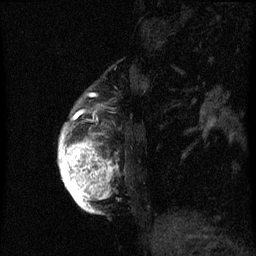
Breast MRI (dynamic contrast-enhanced), one sagittal slice. Slice 11 of 60 in the series (ordered by position). Dynamic contrast-enhanced series, image 2 of 3 at this slice position (ordered by acquisition). 1.5 T. TE 4.2 ms, TR 8 ms. 2 mm slice thickness. 256 × 256 image matrix, field of view 180 × 180 mm. Female patient, age 56 years.
Outlined on this slice (semi-automatic segmentation, software-assisted and operator-edited):
- analysis volume of interest (the breast-tissue region the enhancement analysis was run in; not a lesion): bounding box (x1, y1, x2, y2) in pixels: (58, 96, 119, 215)
- tumour enhancement mask (voxels above the 70 % enhancement threshold inside the analysis volume of interest): (58, 110, 113, 213)